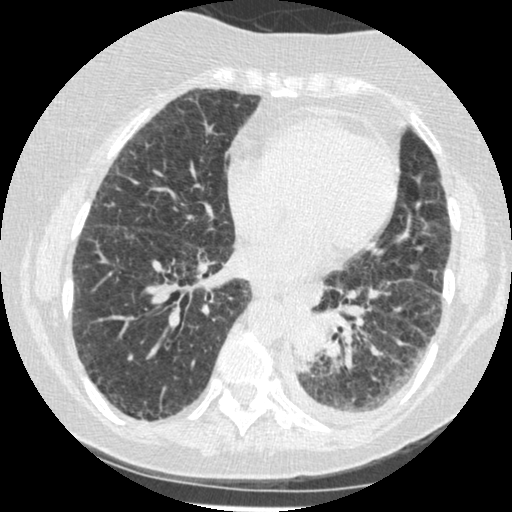
Low-dose screening chest CT, one axial slice; 120 kVp; lung window (W 1500 / L -600 HU); 1.25 mm slice thickness; 512 × 512 image matrix, field of view 310 × 310 mm.
Outlined on this slice (expert manual segmentation):
- lesion 1 (tumor, lower lobe of left lung): bounding box (x1, y1, x2, y2) in pixels: (291, 319, 323, 372)